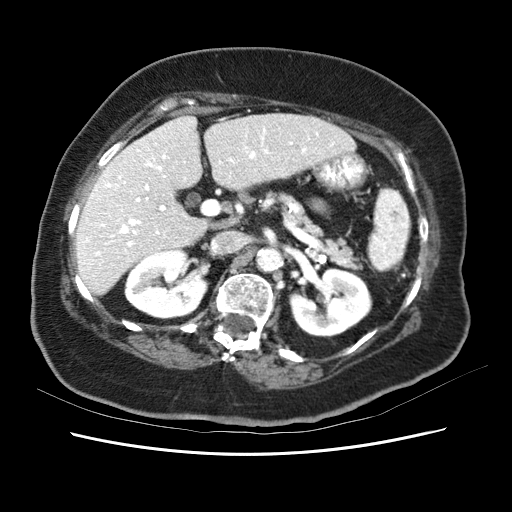
Contrast-enhanced abdominal CT (liver protocol), one axial slice; slice 30 of 62 in the series (ordered by position); reconstruction kernel STANDARD; 120 kVp; soft-tissue window (W 400 / L 40 HU); 2.5 mm slice thickness; 512 × 512 image matrix, field of view 340 × 340 mm. Case-level facts recorded for this patient, not image findings: diagnosis: hepatocellular carcinoma (patient treated with transarterial chemoembolisation; whether this scan precedes or follows treatment is not stated here); TNM stage (as recorded): Stage-I; Child-Pugh class: B.
Structures marked on this image (semi-automatic segmentation, software-assisted and operator-edited):
- liver parenchyma outside the tumour (the mass and vessels are separate outlines, so this box may not span the whole liver): bounding box <76,112,358,298> (left, top, right, bottom; pixels)
- liver vessels: <78,118,332,269>